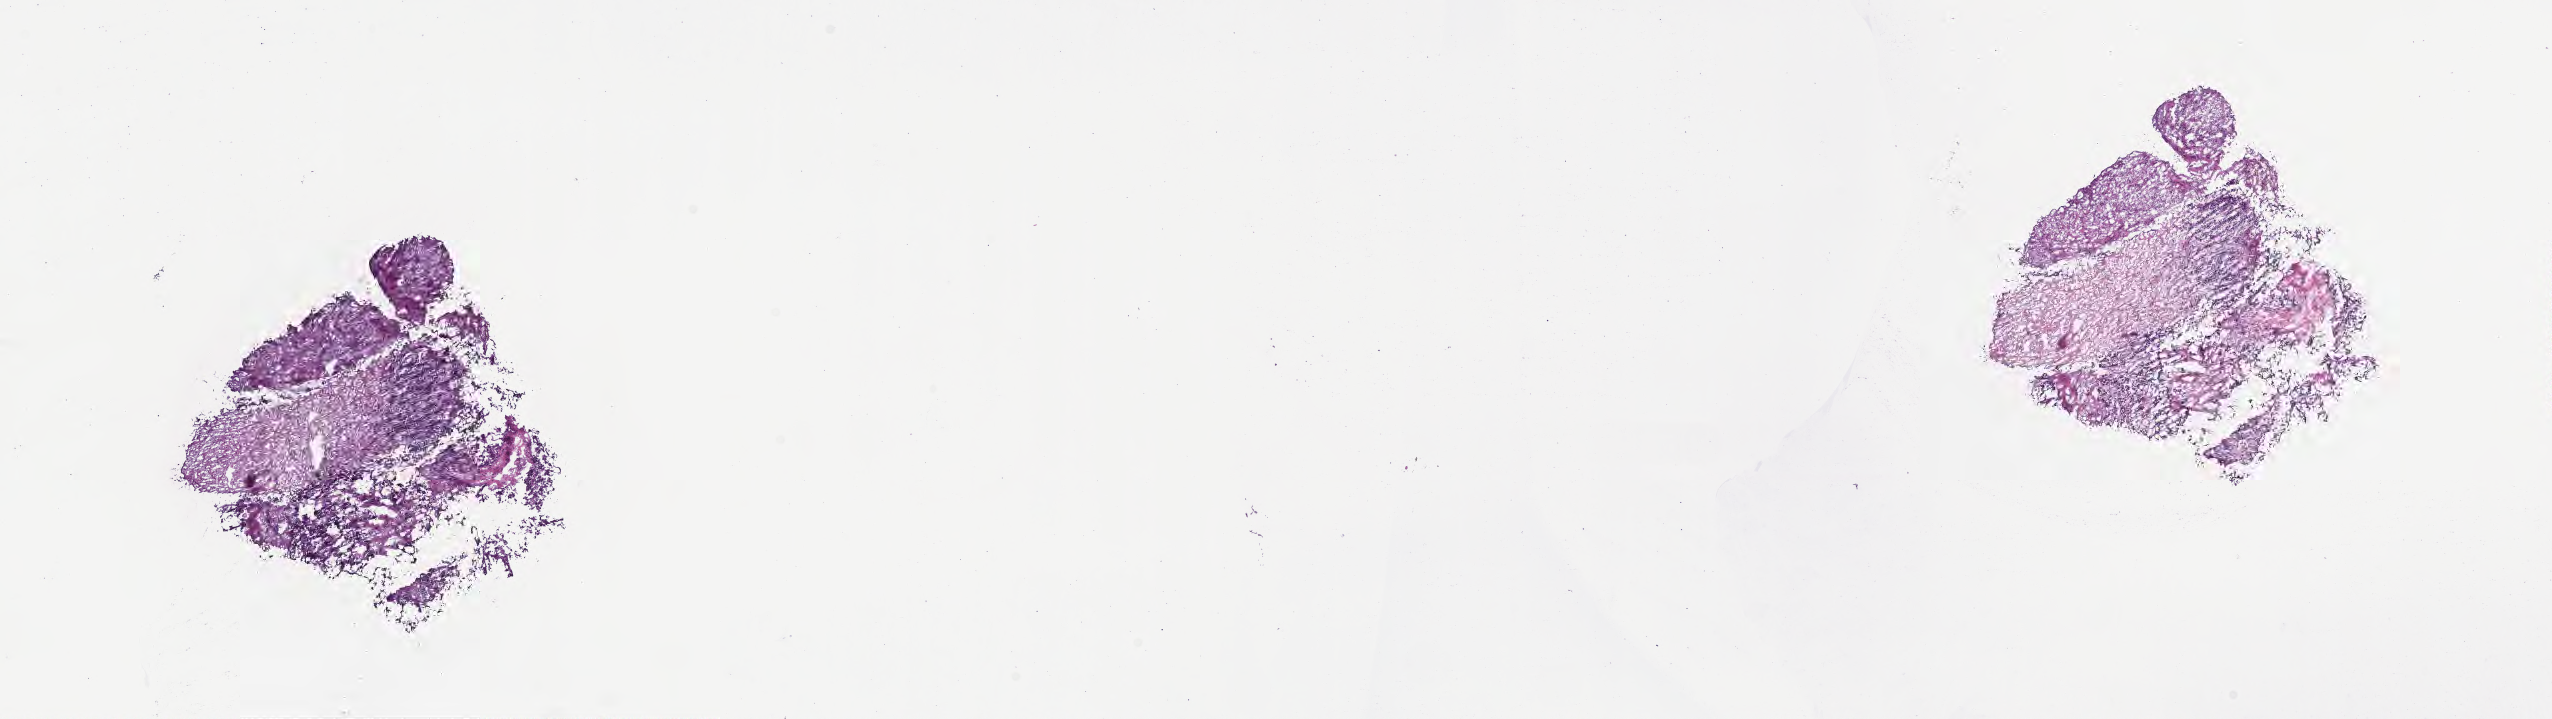
Digitized H&E-stained section of tumor tissue from the adrenal gland — a low-resolution overview of the entire scanned area, about 20.6 x 5.8 mm; cryosection (OCT / tissue freezing medium). Male patient, age 132 months (11 years).
Diagnosis (ICD-O-3 morphology term): Neuroblastoma, NOS.